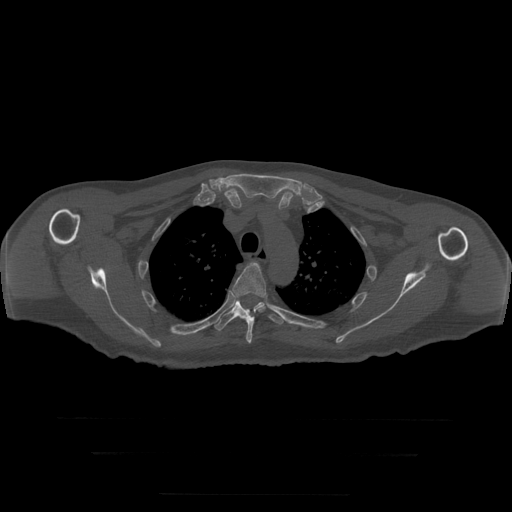
CT including the spine, one axial slice; slice 236 of 397 in the series (ordered by position); reconstruction kernel STANDARD; 120 kVp; bone window (W 1800 / L 400 HU); 1.25 mm slice thickness; 512 × 512 image matrix, field of view 510 × 510 mm. Patient age 73 years. Case-level facts recorded for this patient, not image findings: primary cancer: prostate.
Annotated regions visible in this slice (semi-automatically segmented with operator editing):
- T4 vertebra: box from (x=233, y=263) to (x=267, y=344) px
- T5 vertebra: (x=215, y=300)–(x=285, y=331)